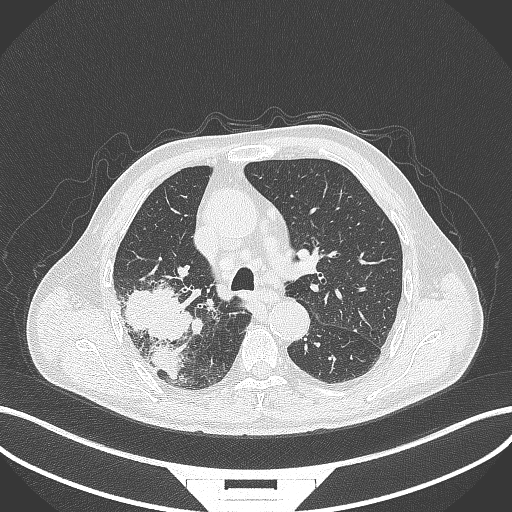
Chest CT, one axial slice; slice 278 of 429 in the series (ordered by position); reconstruction kernel B70f; 120 kVp; lung window (W 1500 / L -600 HU); 1 mm slice thickness; 512 × 512 image matrix, field of view 400 × 400 mm. Patient: male, 72 years. Case-level facts recorded for this patient, not image findings: clinical TNM (as recorded): T3 N2 M0.
Annotated regions visible in this slice (bounding box drawn by a radiologist):
- lung tumour (recorded histology: adenocarcinoma): bounding box (x1, y1, x2, y2) in pixels: (117, 283, 194, 383)